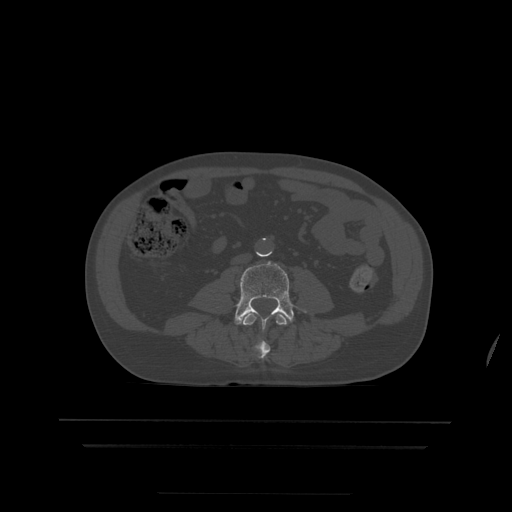
CT including the spine, one axial slice. Position 102 of 522 along the scan axis. Bone window (W 1800 / L 400 HU). 1.25 mm slice thickness. 512 × 512 image matrix. Patient age 68 years. Case-level facts recorded for this patient, not image findings: primary cancer: urothelial.
Structures marked on this image (semi-automatically segmented with operator editing):
- L3 vertebra: bounding box [x1, y1, x2, y2] px = [241, 313, 289, 360]
- L4 vertebra: [235, 261, 294, 330]